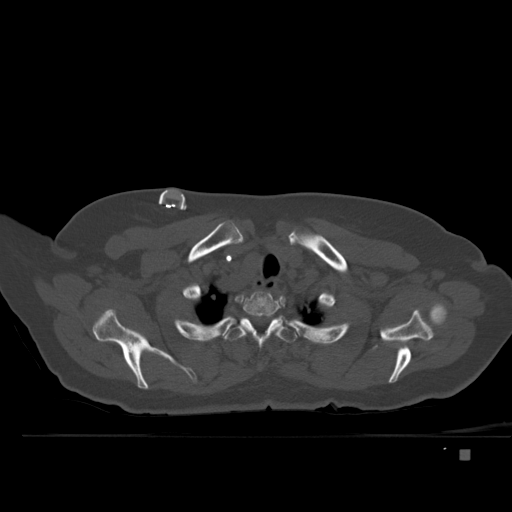
CT including the spine, one axial slice. Slice 396 of 477 in the series (ordered by position). Bone window (W 1800 / L 400 HU). 512 × 512 image matrix, field of view 422 × 422 mm. Female patient, age 74 years. From the clinical record (not read from this slice): primary cancer: colon.
Annotated regions visible in this slice (semi-automatically segmented with operator editing):
- T1 vertebra: bounding box <226,292,283,328> (left, top, right, bottom; pixels)
- T2 vertebra: <198,314,315,351>